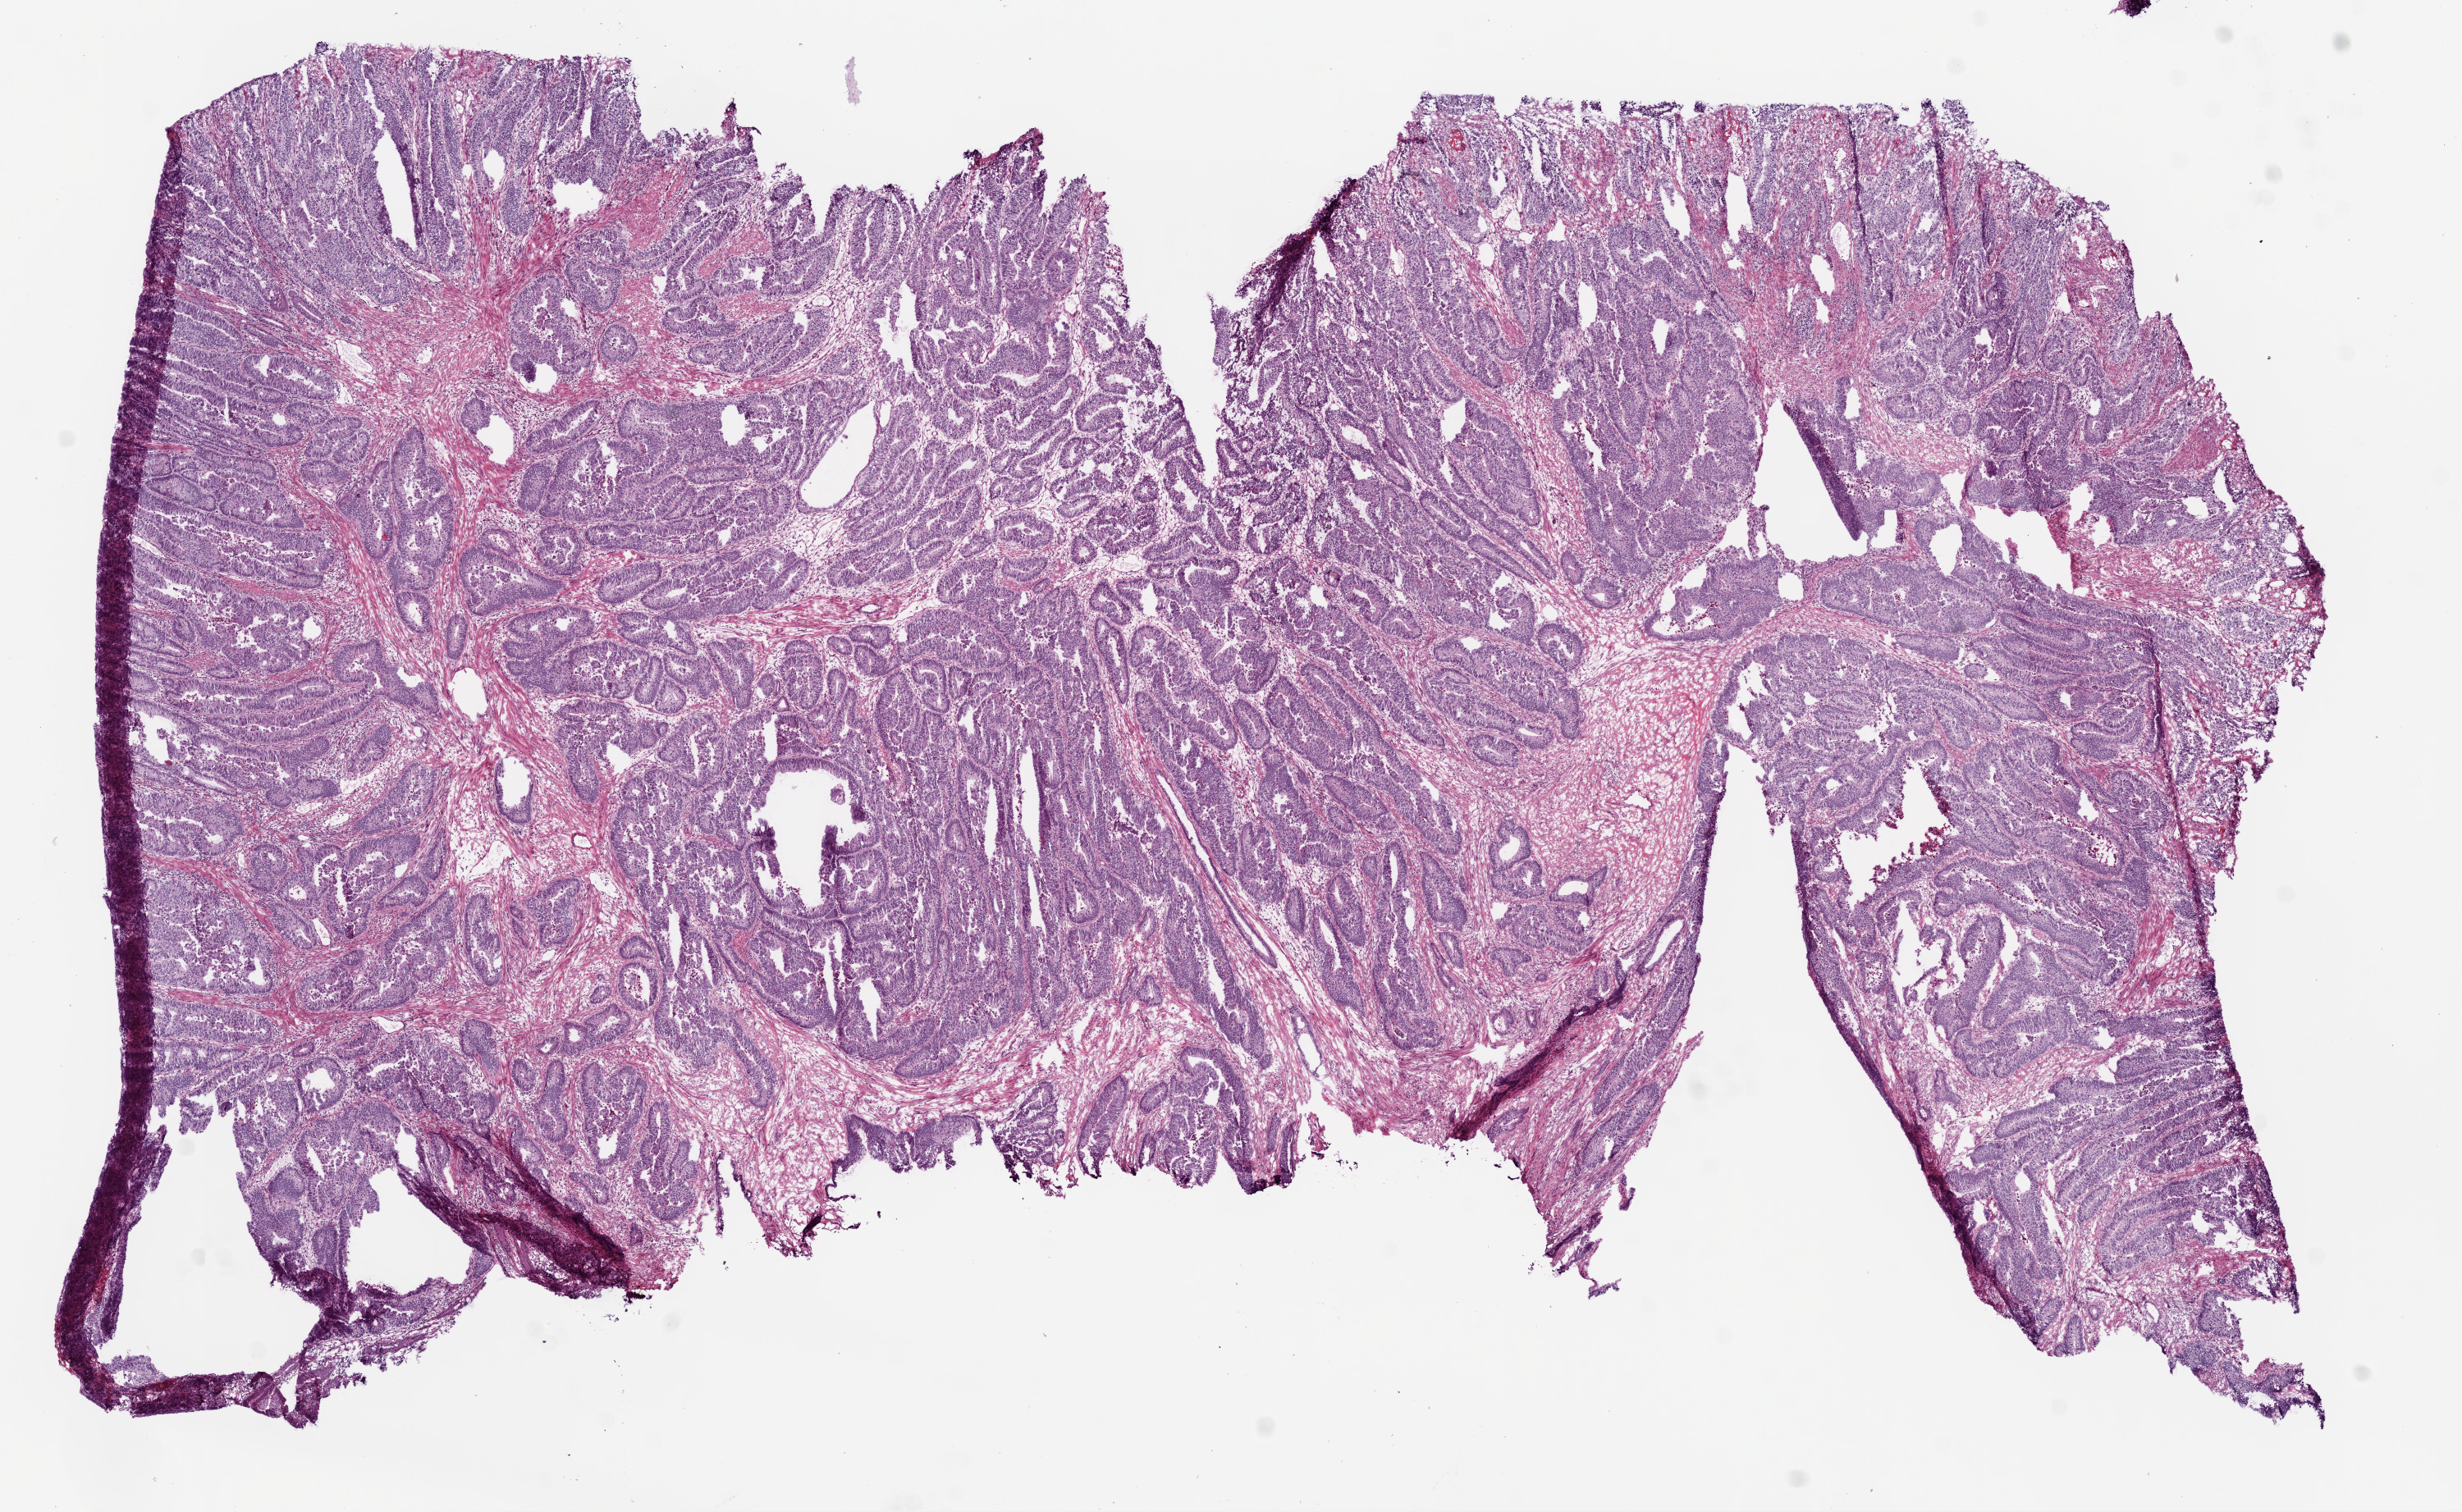
Digitized H&E-stained tissue section (whole slide) — whole scanned area (about 12.0 x 7.4 mm) shown as a low-resolution overview. Frozen section. Primary tumour sample from the colon. Female patient; age at initial diagnosis 63 years. Pathologist review of this section (percent, as recorded): tumour cells 82%, tumour nuclei 80%, normal cells 0%, stromal cells 15%, necrosis 3%.
Pathologic diagnosis: Adenocarcinoma, NOS (cecum). AJCC pathologic stage: IV (6th edition).